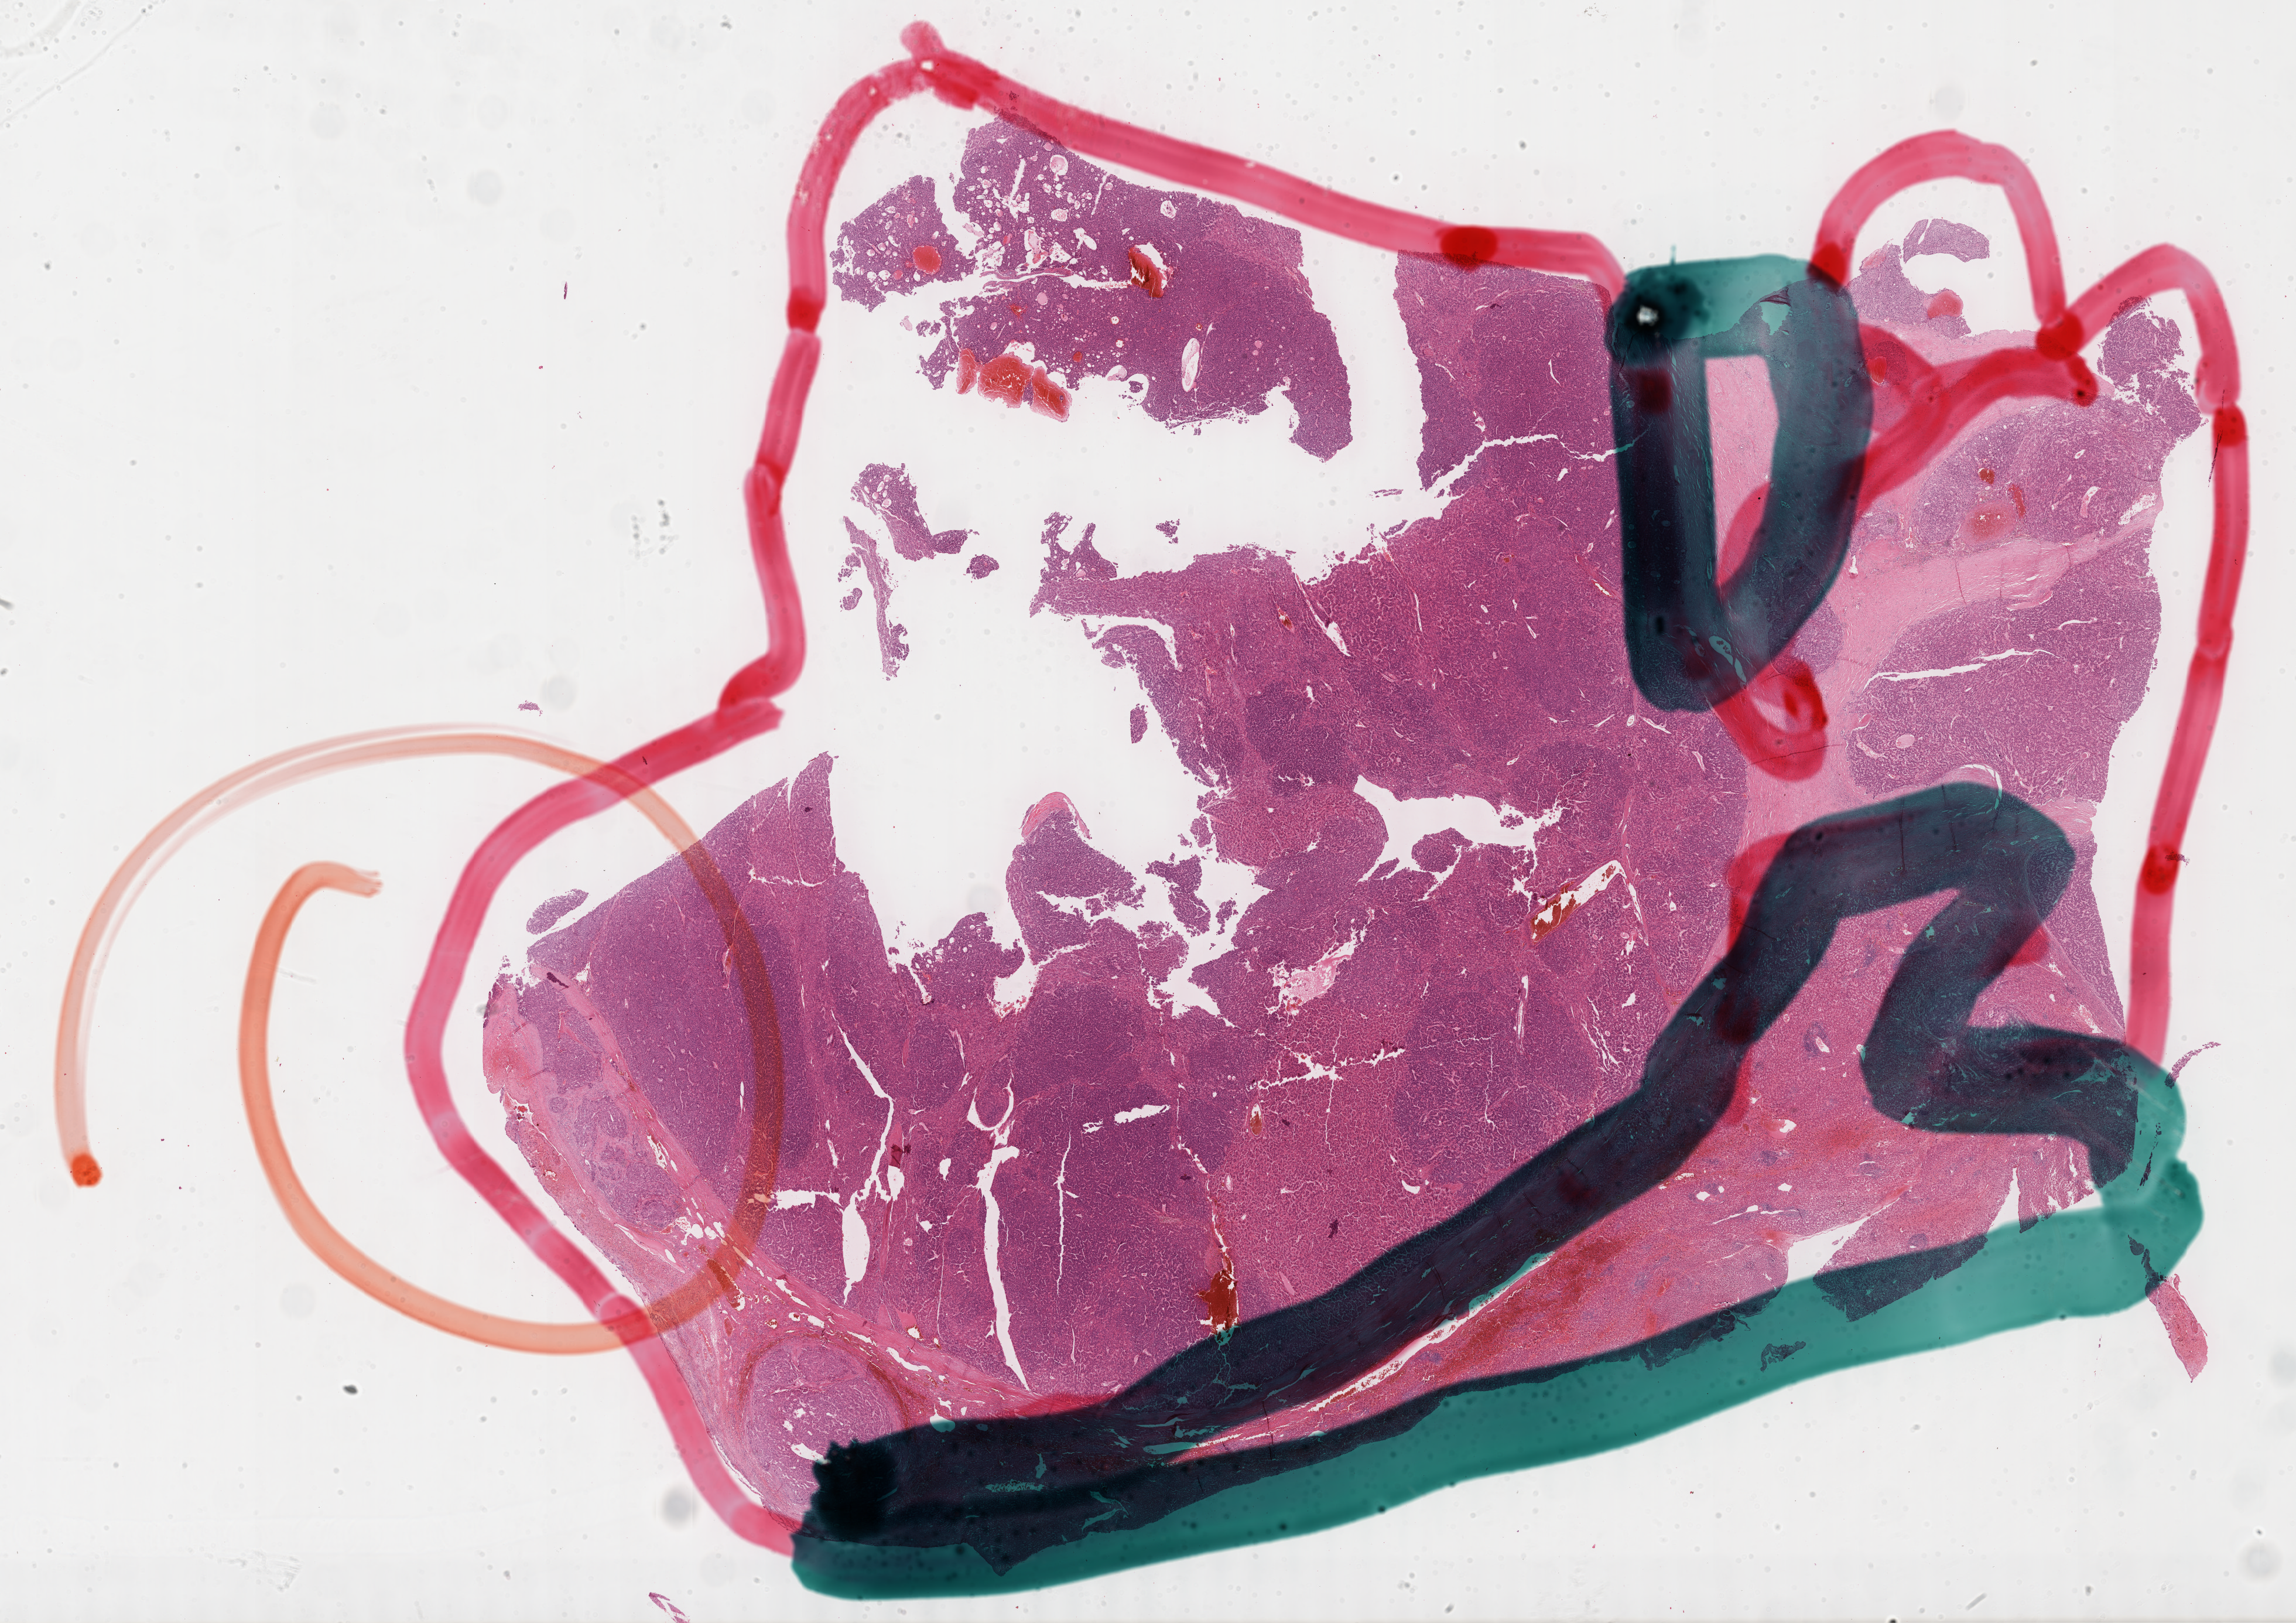
Whole-slide histology image, H&E-stained — low-resolution overview of the scanned area, about 31.7 x 22.4 mm; FFPE section; sample: primary tumour, liver. Patient: male, age at initial diagnosis 29 years.
Pathologic diagnosis: Hepatocellular carcinoma, NOS.